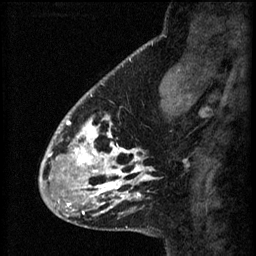
Breast MRI (dynamic contrast-enhanced), one sagittal slice; slice 17 of 60 in the series (ordered by position); 3 images stored at this slice position (order not interpretable as contrast timing); 1.5 T; TE 4.2 ms, TR 8.2 ms; 2.2 mm slice thickness; 256 × 256 image matrix. Patient: female, 41 years.
Annotated regions visible in this slice (semi-automatically segmented with operator editing):
- analysis volume of interest (the breast-tissue region the enhancement analysis was run in; not a lesion): bounding box (x1, y1, x2, y2) in pixels: (56, 104, 157, 207)
- tumour enhancement mask (voxels above the 70 % enhancement threshold inside the analysis volume of interest): (56, 104, 157, 207)